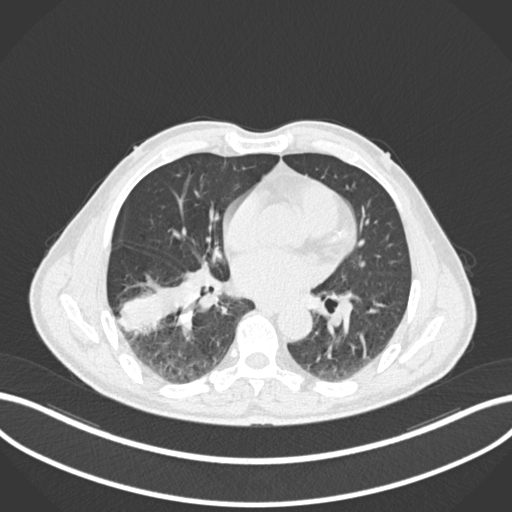
Chest CT, one axial slice; position 88 of 208 along the scan axis; 120 kVp; lung window (W 1500 / L -600 HU); 1 mm slice thickness; 512 × 512 image matrix. Male patient, age 58 years. Case-level facts recorded for this patient, not image findings: clinical TNM (as recorded): T3 N0 M0; histopathological grade: G2.
Outlined on this slice (bounding box drawn by a radiologist):
- lung tumour (recorded histology: squamous cell carcinoma): bounding box (x1, y1, x2, y2) in pixels: (119, 281, 194, 340)